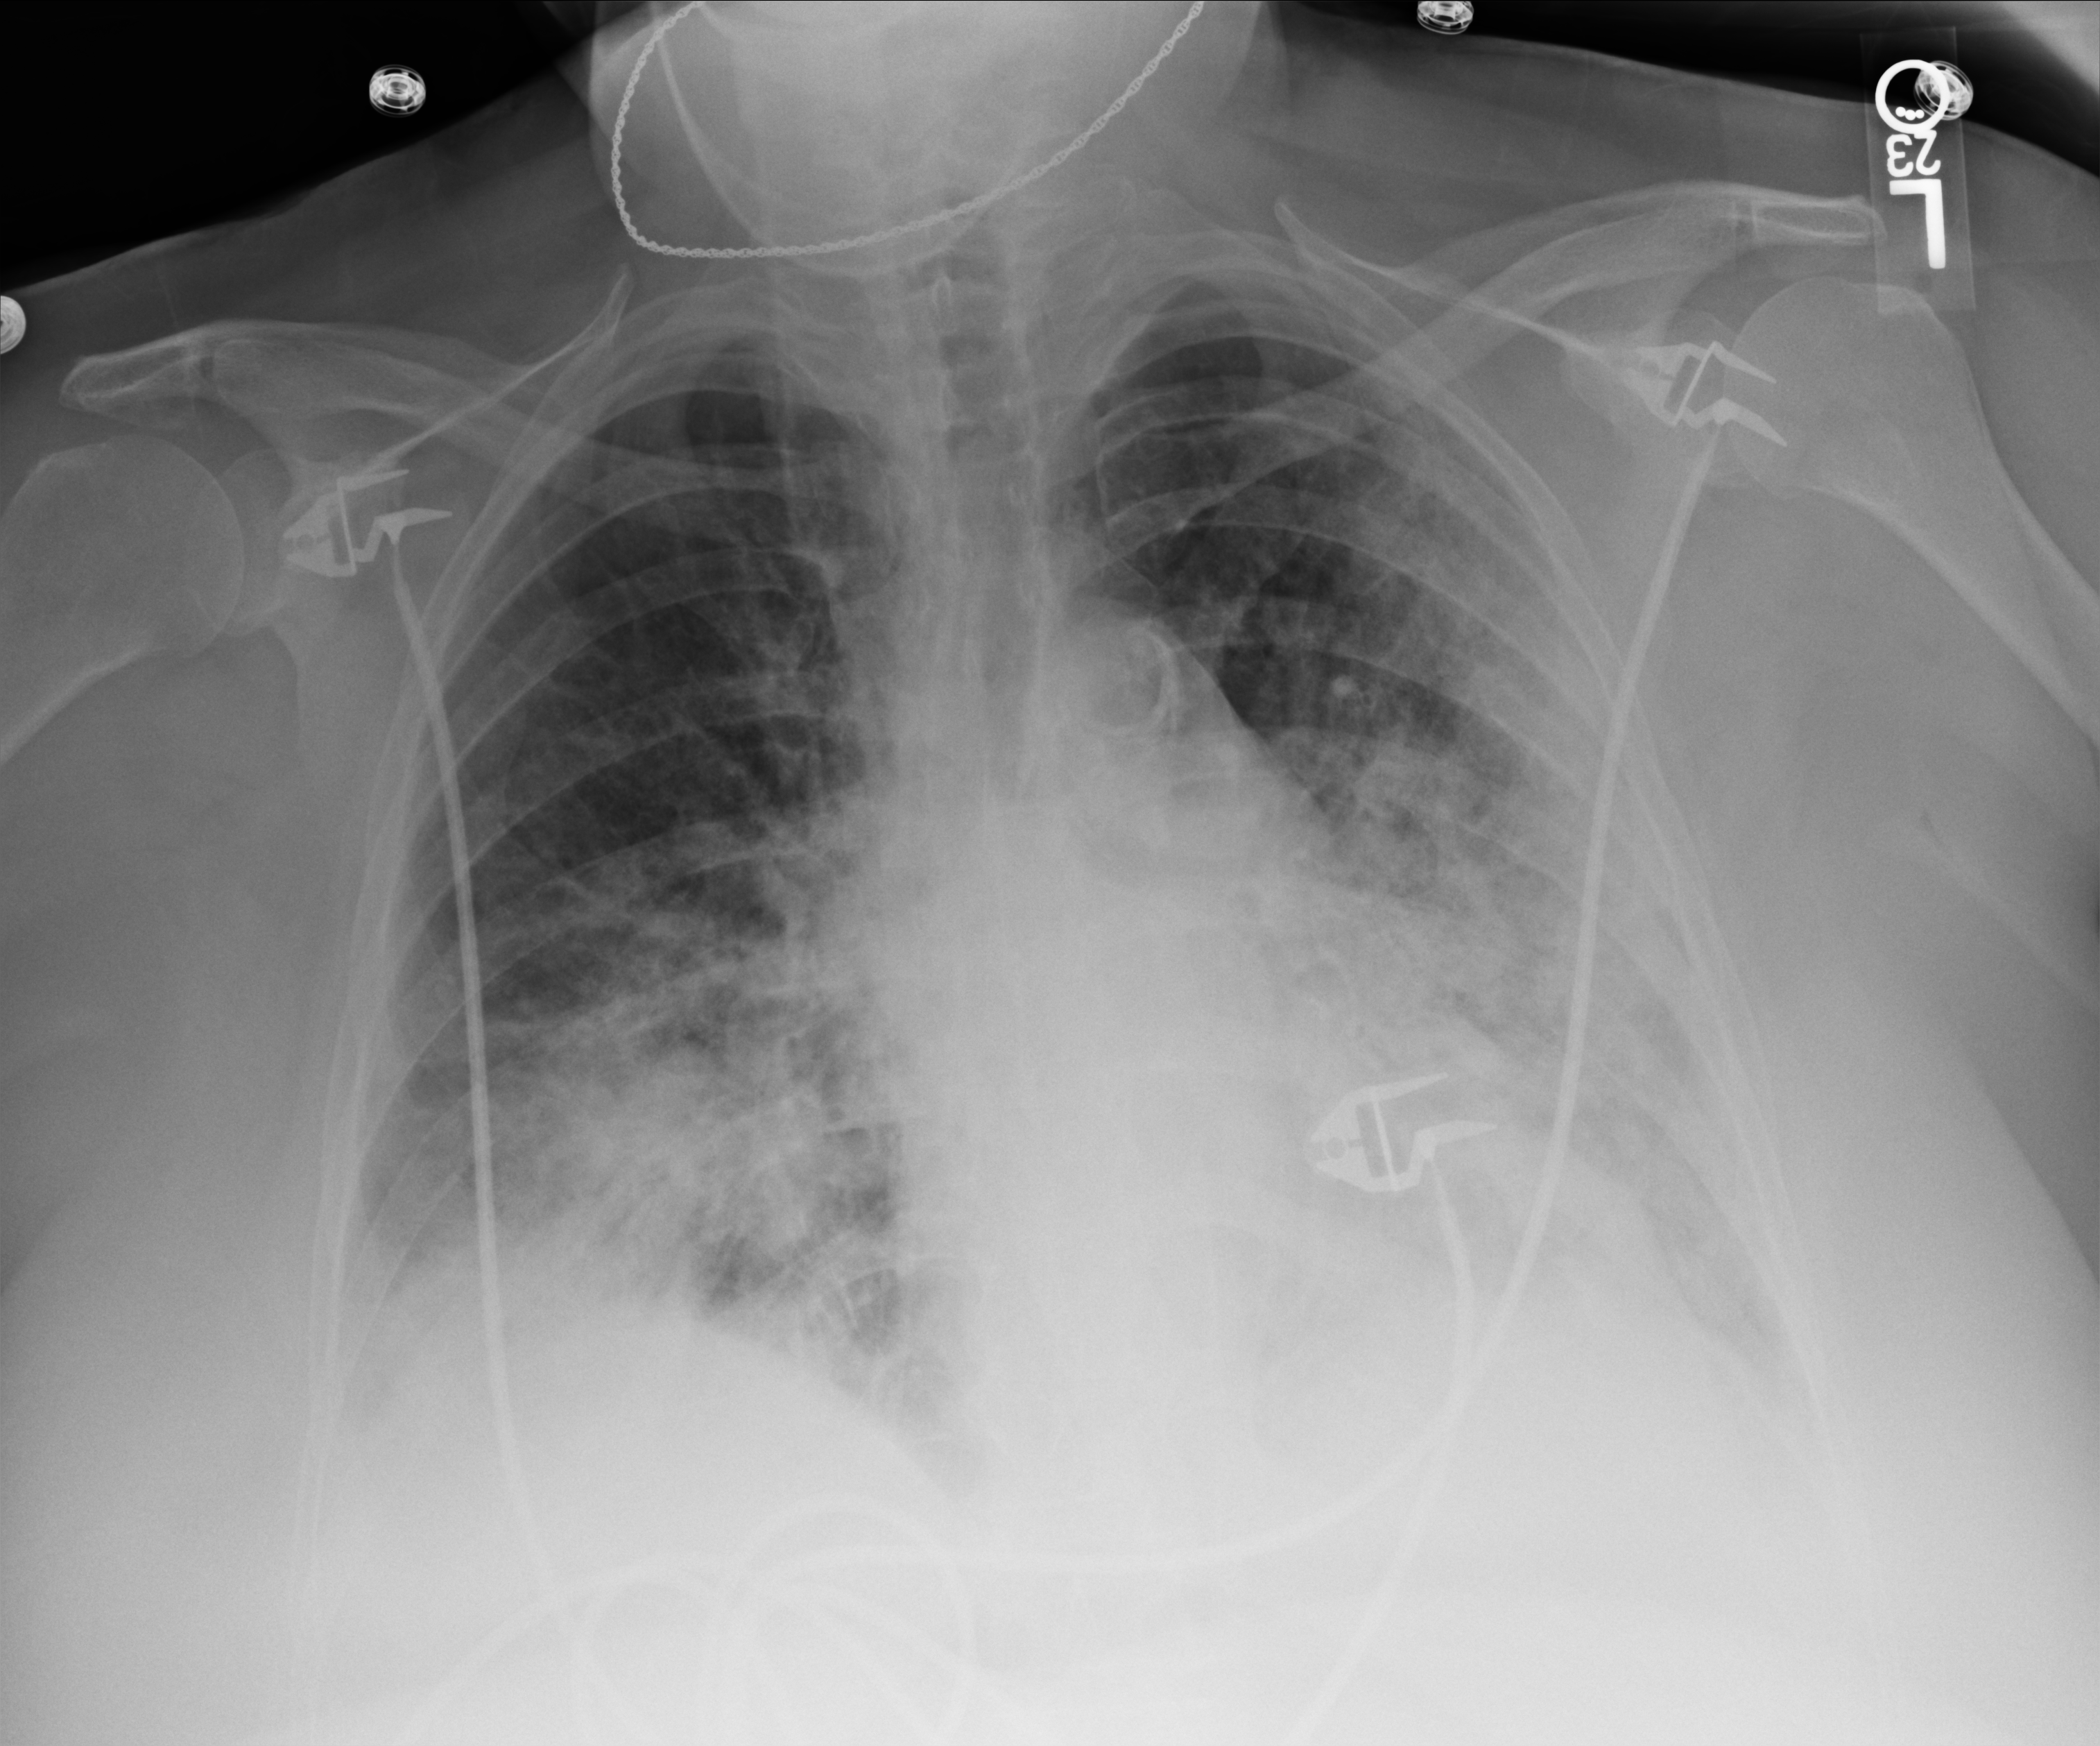
Portable chest radiograph. Patient hospitalised with COVID-19; female, aged 60–74 years.
Hospital-stay facts (about this admission, not read from this image; timing relative to this image not recorded): diabetes (admission record): yes; mechanically ventilated during this hospital stay: no.